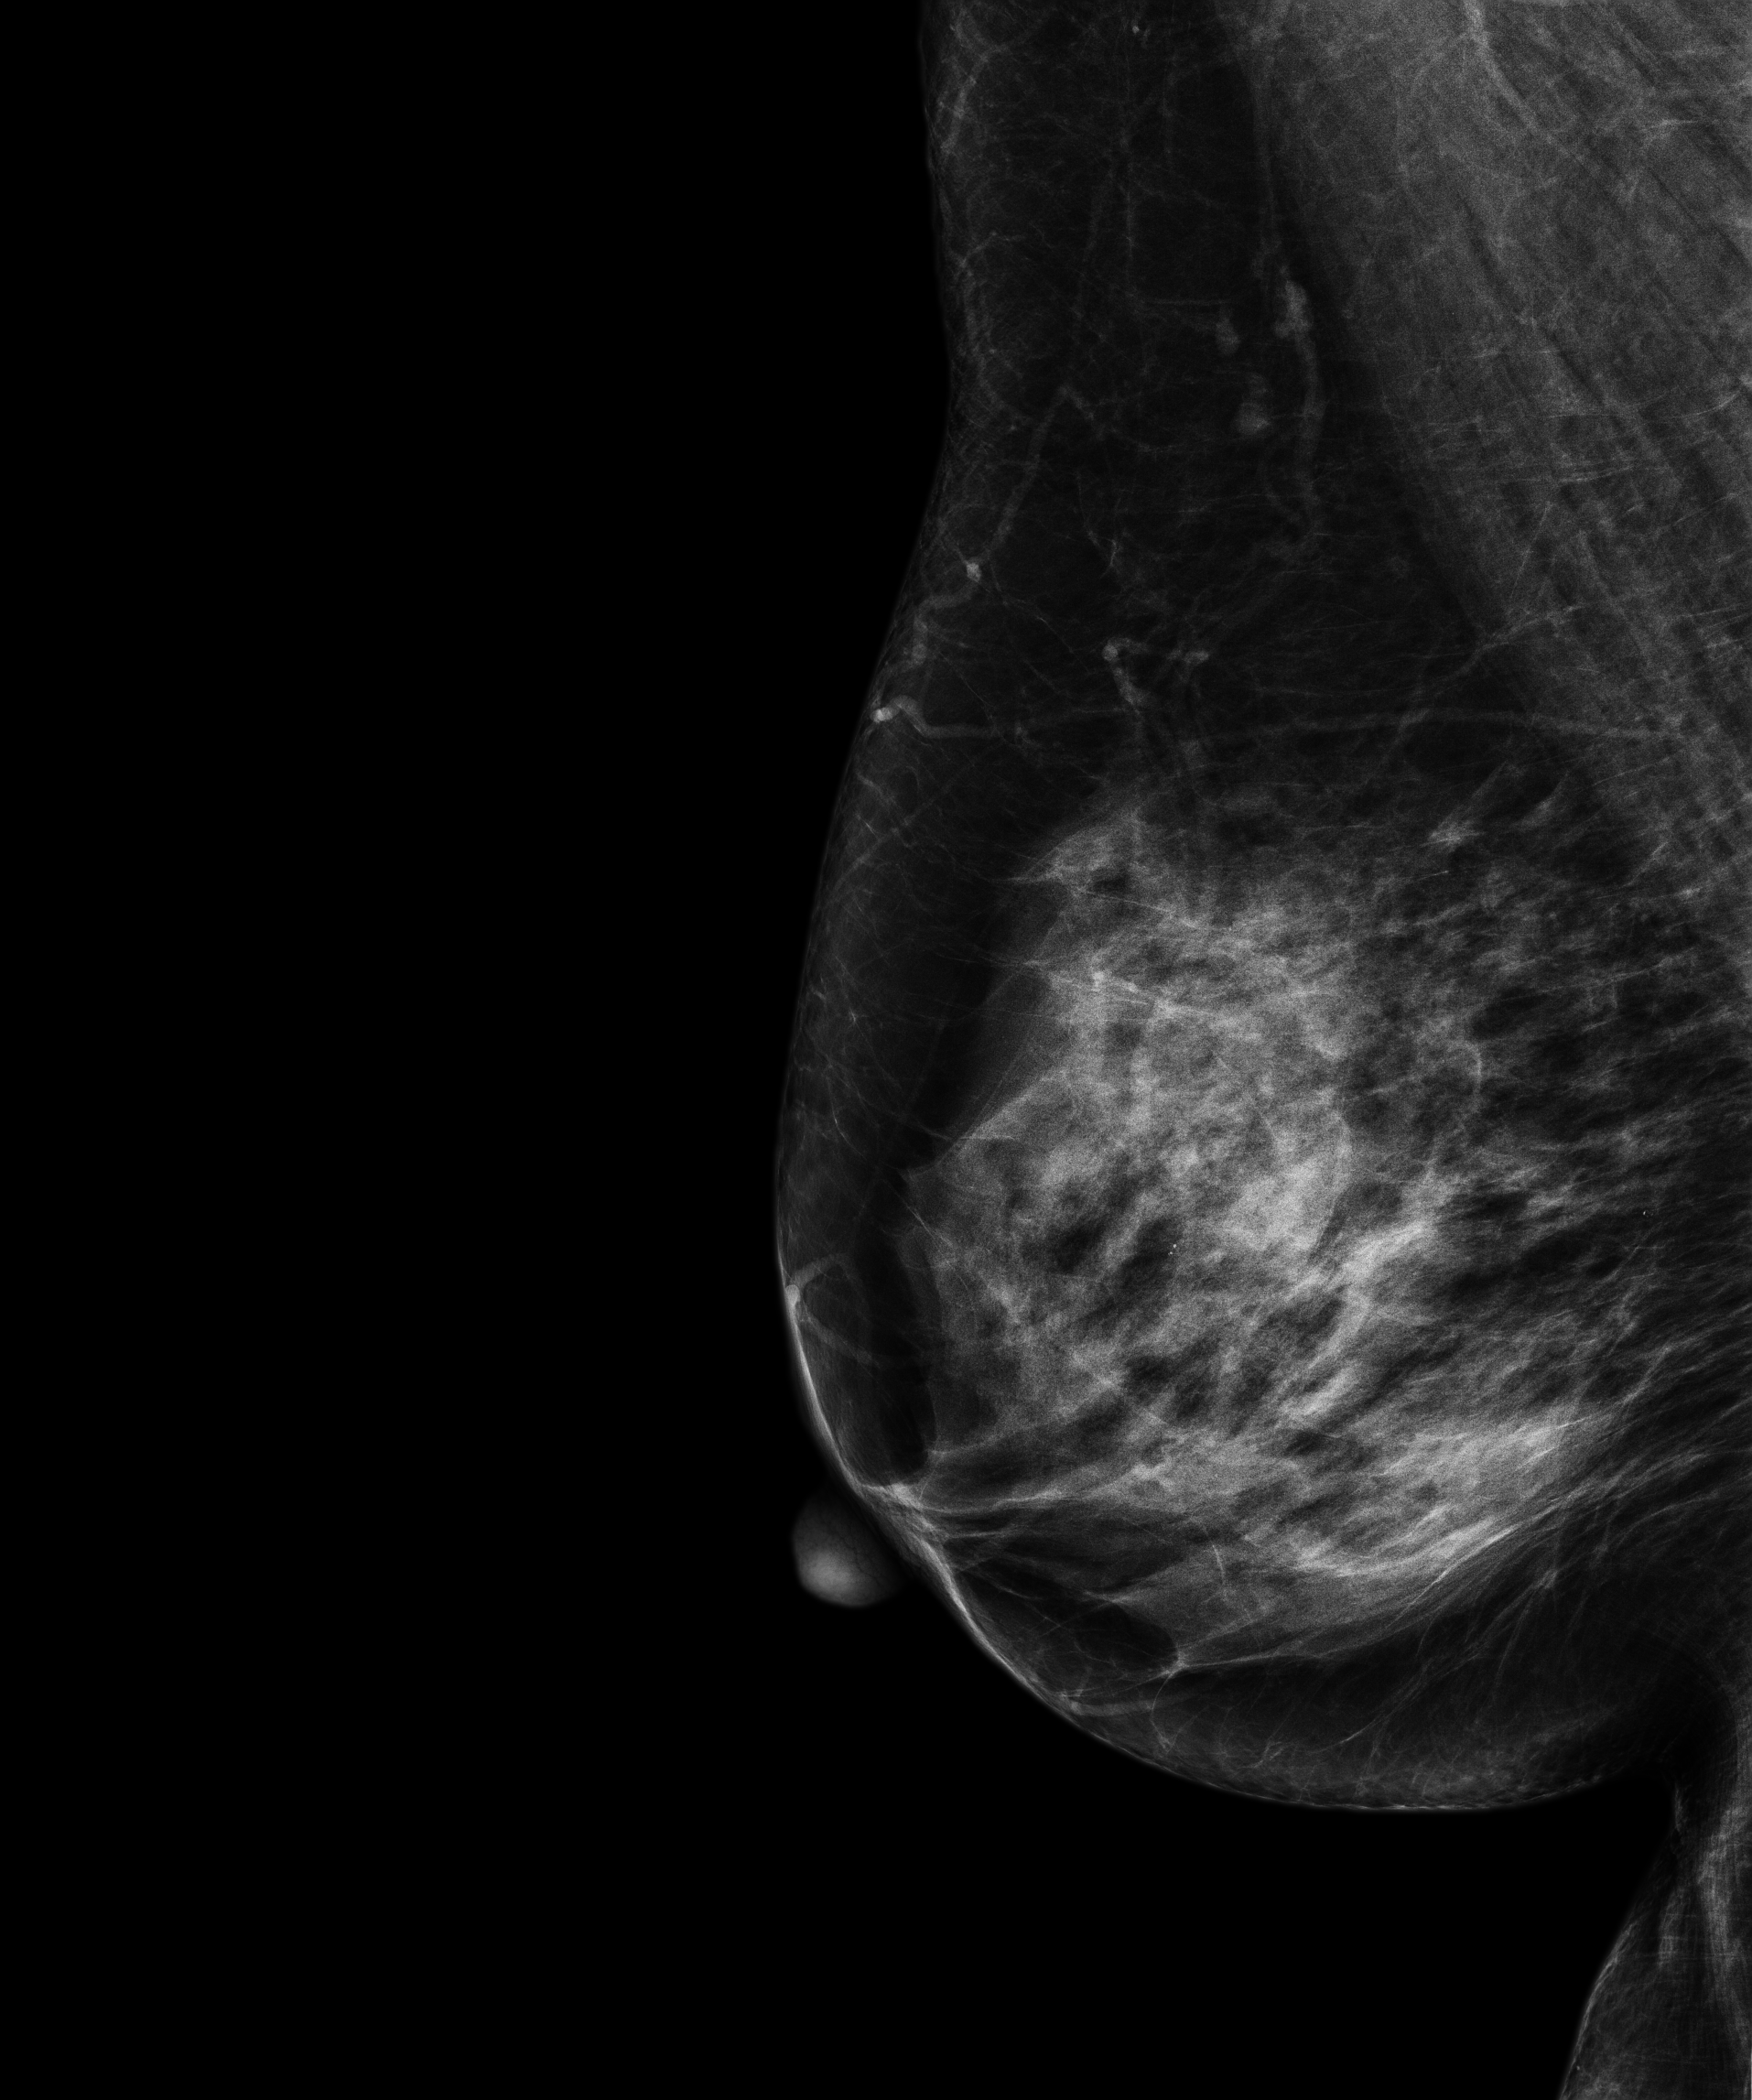
Annual screening mammography examination, compressed breast thickness 59.7 mm. Patient: female, 68 years.
Image type: full-field digital mammogram. Breast: right. Projection: mediolateral oblique (MLO) view.